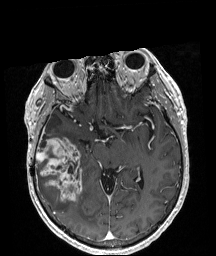
Brain MRI from a brain-tumour surgery series, one axial slice. Position 115 of 208 along the scan axis. T1-weighted post-contrast. 1 mm slice thickness. 216 × 256 image matrix. Case-level facts recorded for this patient, not image findings: histopathology: Astrocytoma; WHO grade: 4; IDH mutation: yes; tumour location: Right Temporal.
Outlined on this slice (expert manual segmentation):
- tumour: bounding box <36,137,82,201> (left, top, right, bottom; pixels)